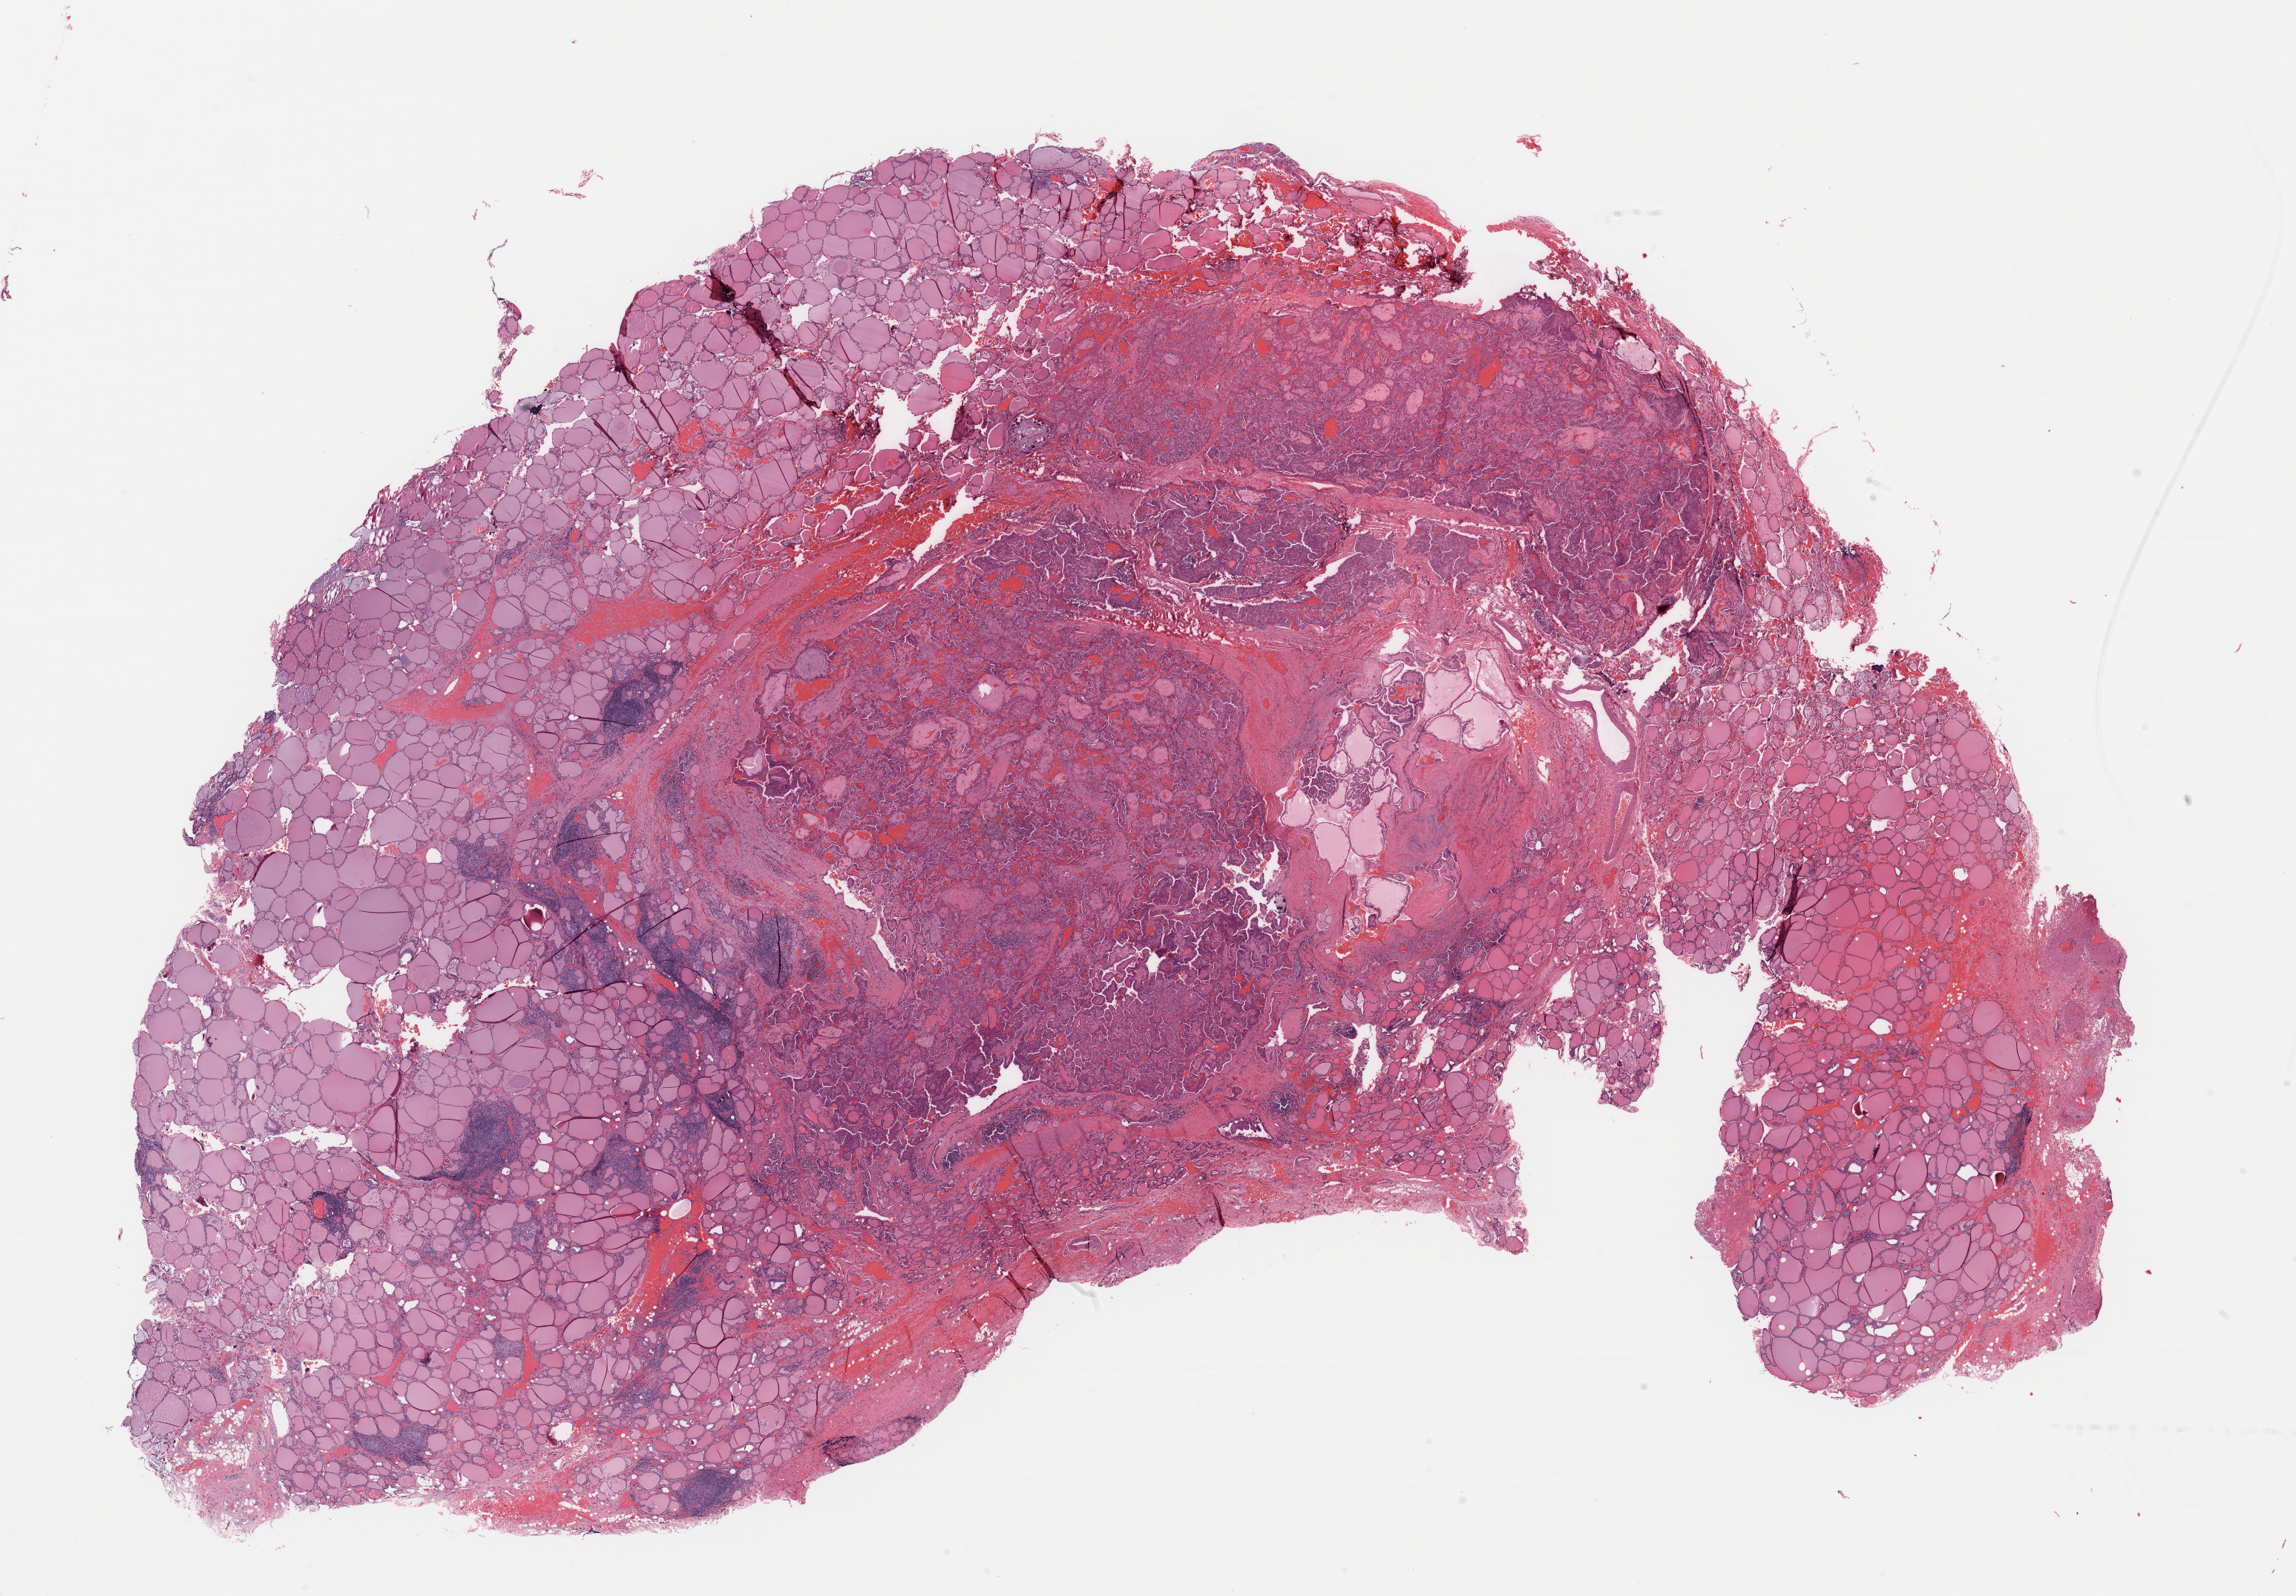
Digitized H&E tissue section (whole slide), whole scanned area (about 24.4 x 17.0 mm, acquisition: 40x scan) shown as a low-resolution overview, formalin-fixed paraffin-embedded (FFPE) diagnostic section, primary tumour sample from the thyroid. Female patient; age at initial diagnosis 38 years.
- pathologic diagnosis: Papillary adenocarcinoma, NOS (thyroid gland)
- AJCC pathologic stage: I (6th edition)
- lymph nodes positive (case pathology): 0 of 1 examined
- TNM: T1 N0 M0